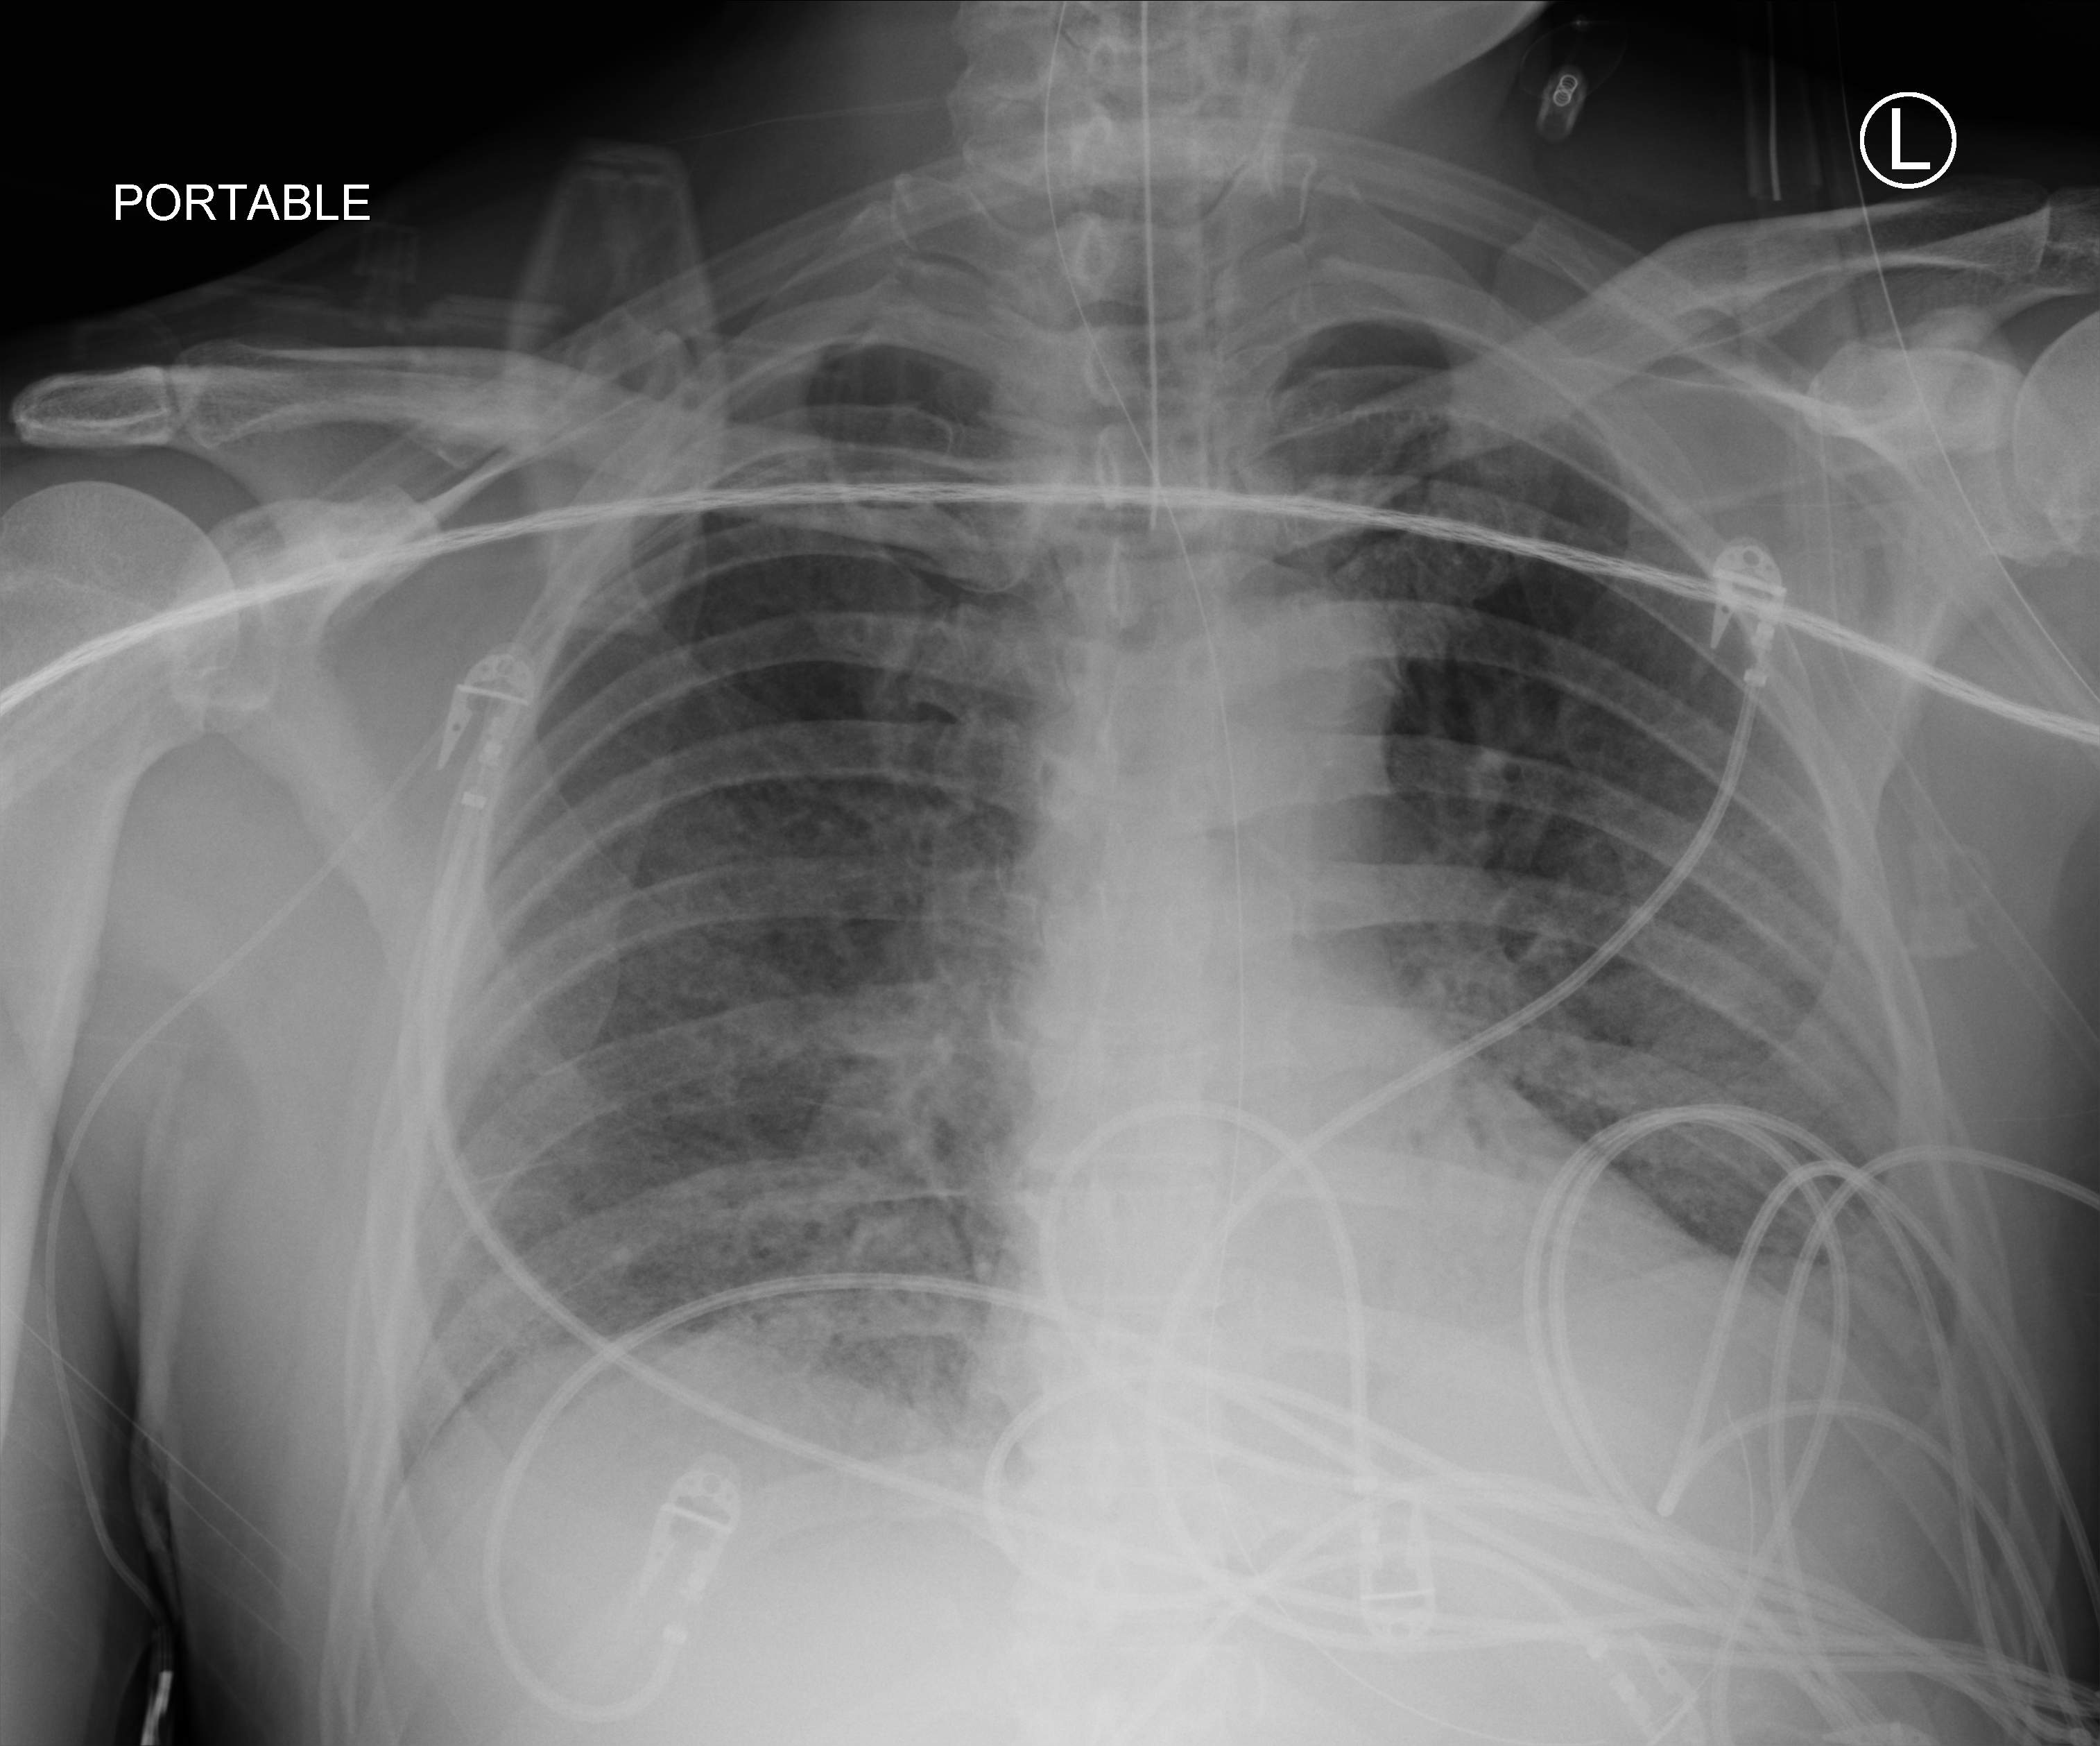
Portable chest radiograph; anteroposterior (AP) projection. Male patient hospitalised with COVID-19, age 60–74 years.
Admission-level facts for this patient (not findings on this image; timing relative to this image not recorded):
- length of hospital stay: 26 days
- admitted to intensive care during this hospital stay: yes
- other chronic lung disease (admission record): no